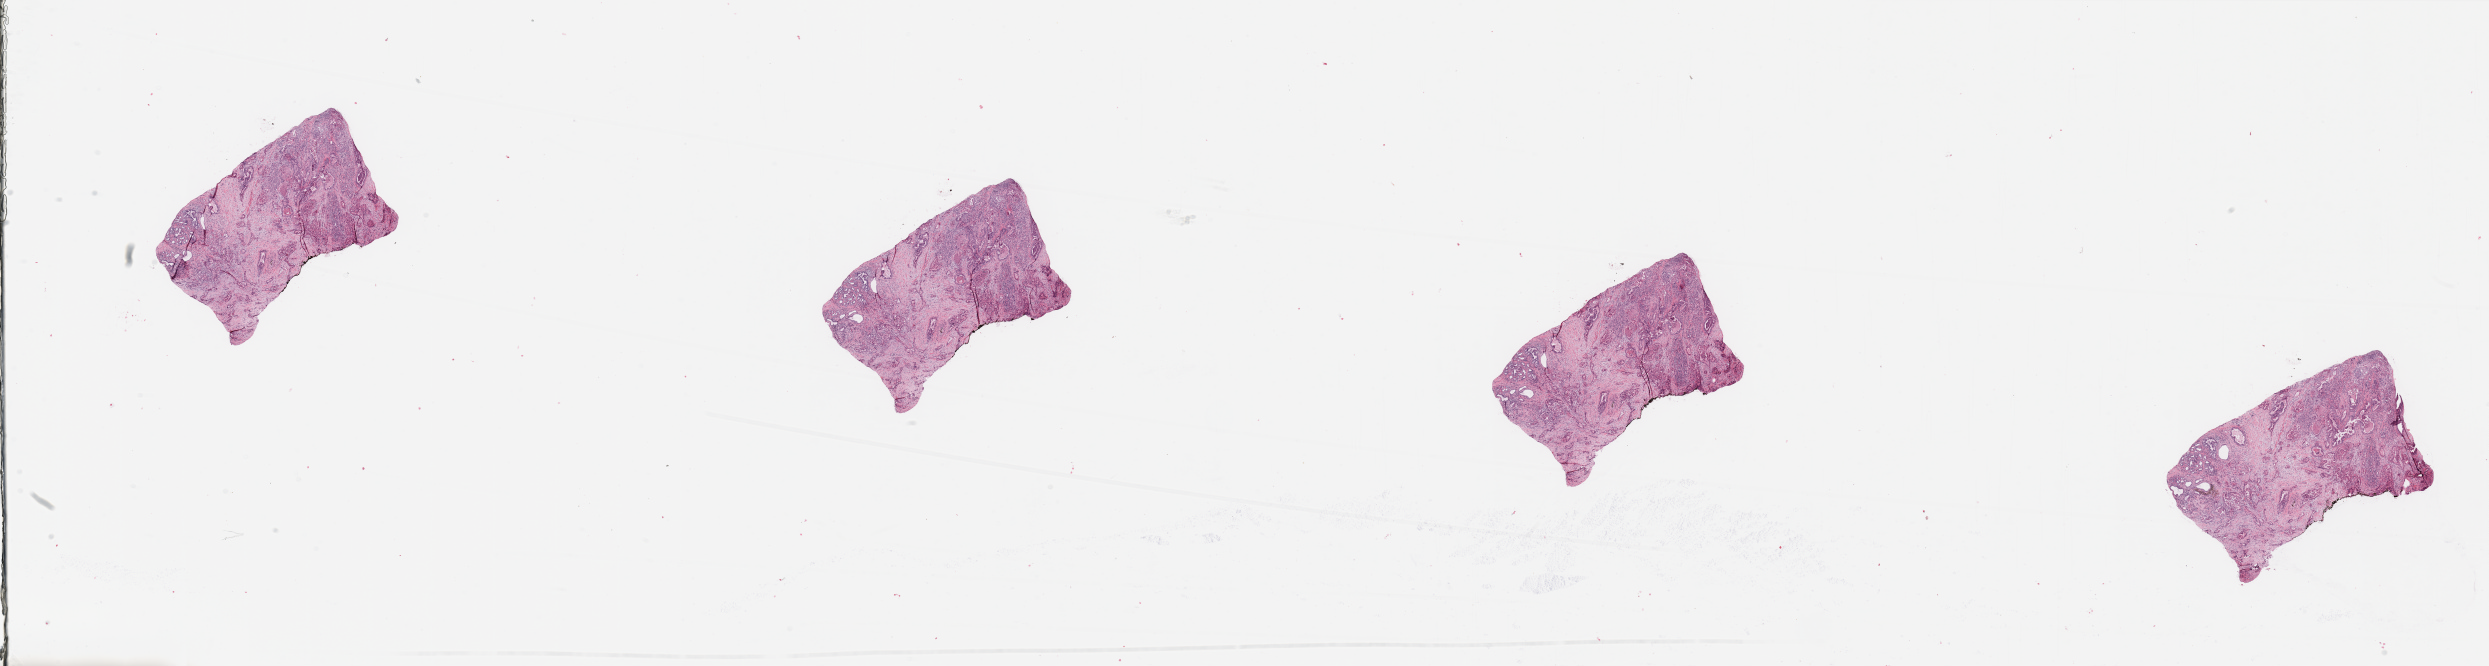
Digitized H&E tissue section (whole slide) — a low-resolution overview of the entire scanned area, about 39.4 x 10.5 mm (acquisition: 20x scan). Tumour tissue sample, sampled site: pancreas. 78-year-old male patient. Histologic grade: G2 (moderately differentiated). Composition of this section per pathologist review: tumour nuclei 40%, necrosis 5%.
• histologic diagnosis: Infiltrating duct carcinoma, NOS
• primary tumour site (as recorded): head
• AJCC pathologic stage: IIB